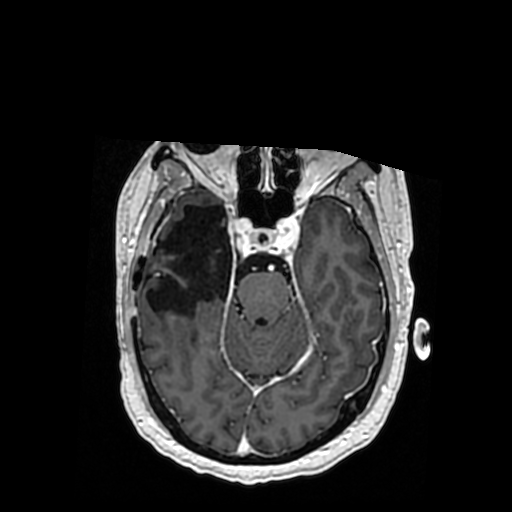
Brain MRI from a brain-tumour surgery series, one axial slice. Position 228 of 364 along the scan axis. T1-weighted post-contrast. 0.5 mm slice thickness. 512 × 512 image matrix. From the clinical record (not read from this slice): histopathology: Oligodendroglioma; WHO grade: 3; IDH mutation: yes; tumour location: Right Posterior Temporal Inferior Parietal.
Structures marked on this image (expert manual segmentation):
- previous resection cavity: box from (x=146, y=205) to (x=232, y=316) px